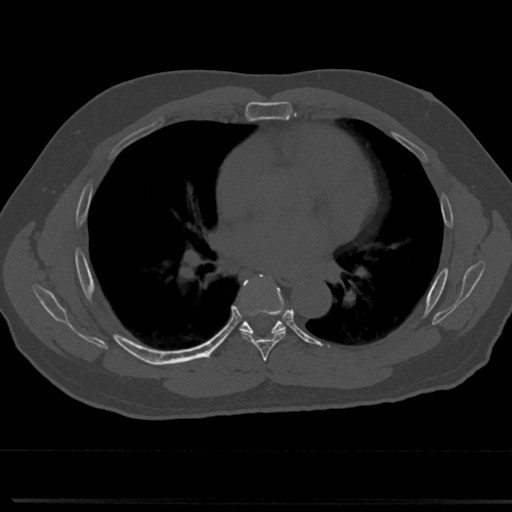
CT including the spine, one axial slice. Slice 434 of 817 in the series (ordered by position). Reconstruction kernel Br40s/3. 120 kVp. Bone window (W 1800 / L 400 HU). 512 × 512 image matrix. Patient: male, 61 years. Case-level facts recorded for this patient, not image findings: primary cancer: prostate.
Annotated regions visible in this slice (semi-automatic segmentation, software-assisted and operator-edited):
- T5 vertebra: box from (x=265, y=369) to (x=272, y=377) px
- T6 vertebra: (x=237, y=277)–(x=303, y=354)
- T7 vertebra: (x=243, y=328)–(x=280, y=333)